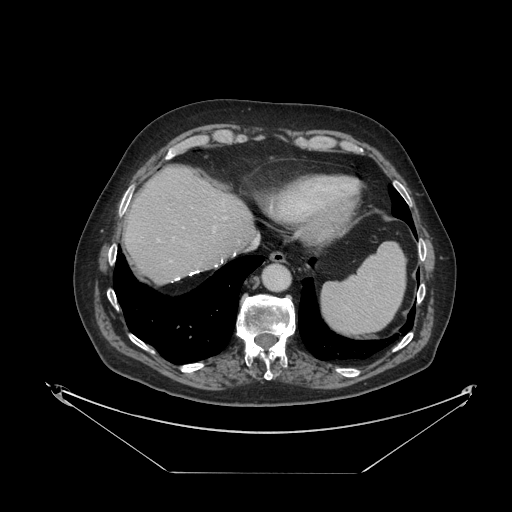
Contrast-enhanced abdominal CT, one axial slice; slice 101 of 121 in the series (ordered by position); intravenous contrast given; soft-tissue window (W 400 / L 40 HU); 2.5 mm slice thickness; 512 × 512 image matrix, field of view 500 × 500 mm. Male patient, age 68 years. Case-level facts recorded for this patient, not image findings: diagnosis: colorectal cancer liver metastases, imaged before liver resection; multiple liver metastases: no; largest metastasis: 4 cm; chemotherapy before resection: yes.
Structures marked on this image (manually delineated by an expert):
- hepatic veins: bounding box (x1, y1, x2, y2) in pixels: (225, 217, 227, 219)
- liver: (125, 168, 254, 282)
- planned liver remnant (the part of the liver to remain after resection): (125, 167, 254, 283)
- portal vein (with intrahepatic branches): (157, 227, 215, 261)